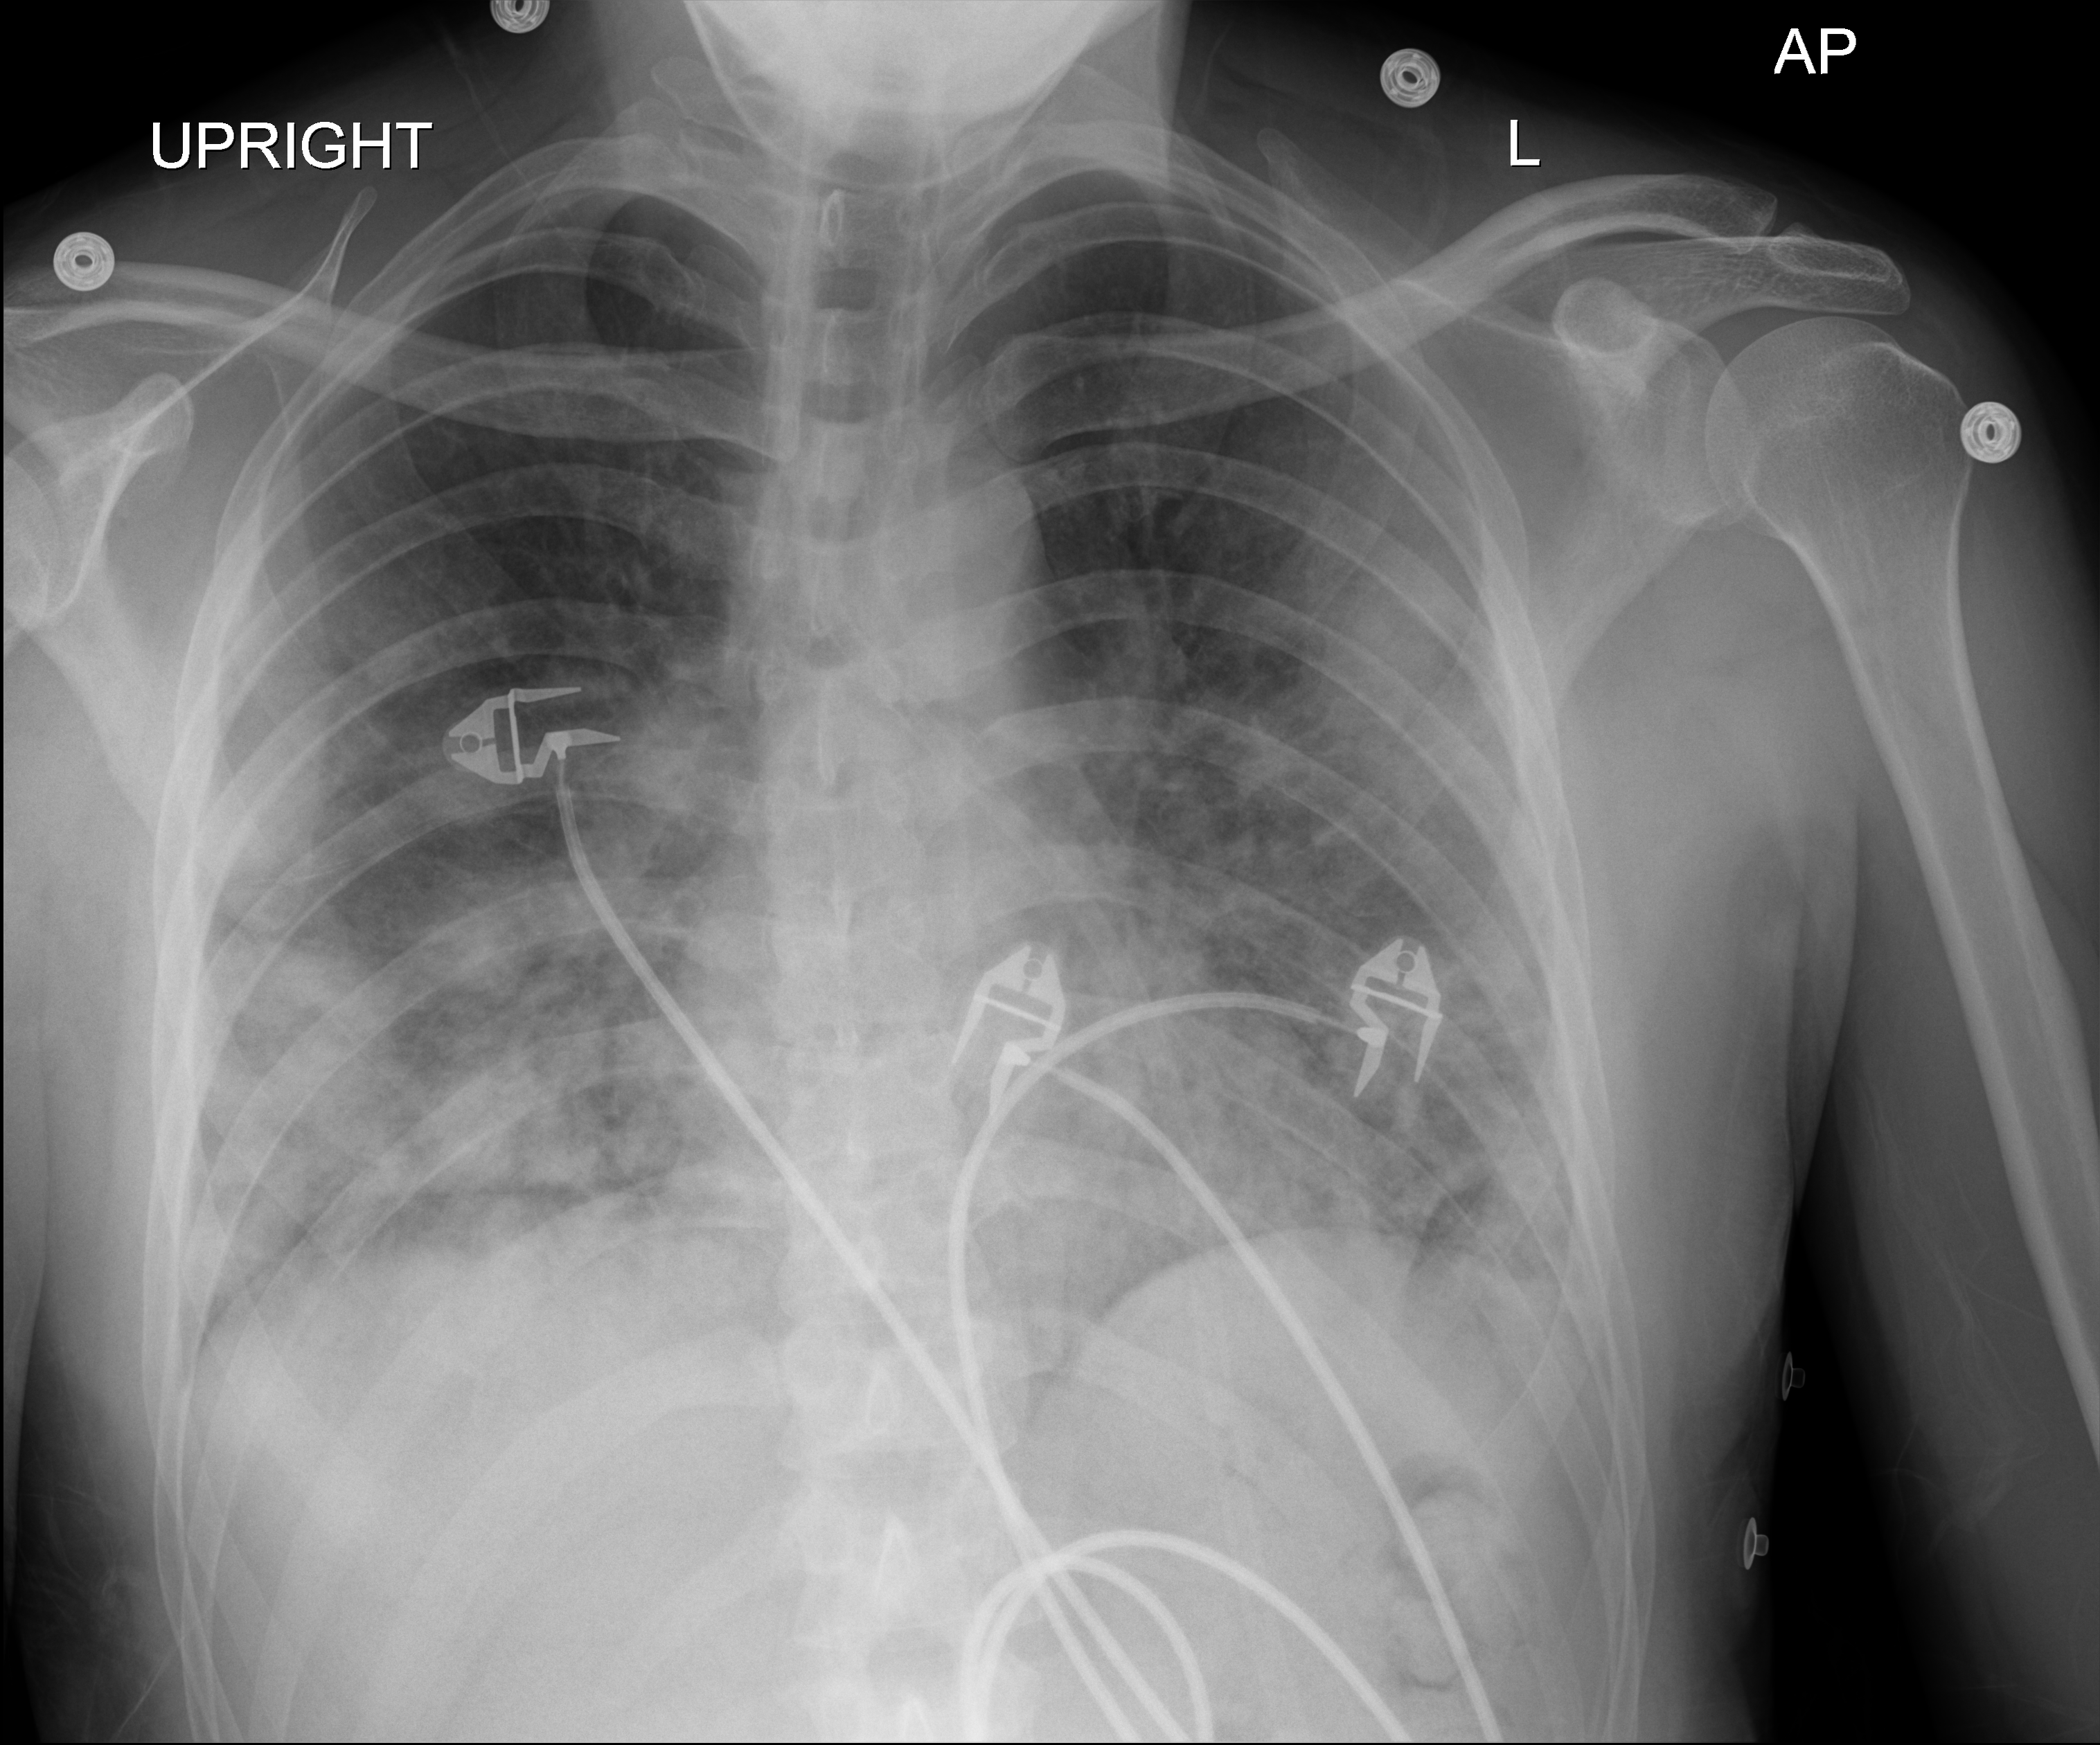
Portable chest radiograph. Patient hospitalised with COVID-19; male, aged 18–59 years.
Admission-level facts for this patient (not findings on this image; timing relative to this image not recorded): mechanically ventilated during this hospital stay: no; chronic kidney disease (admission record): no; admitted to intensive care during this hospital stay: no.